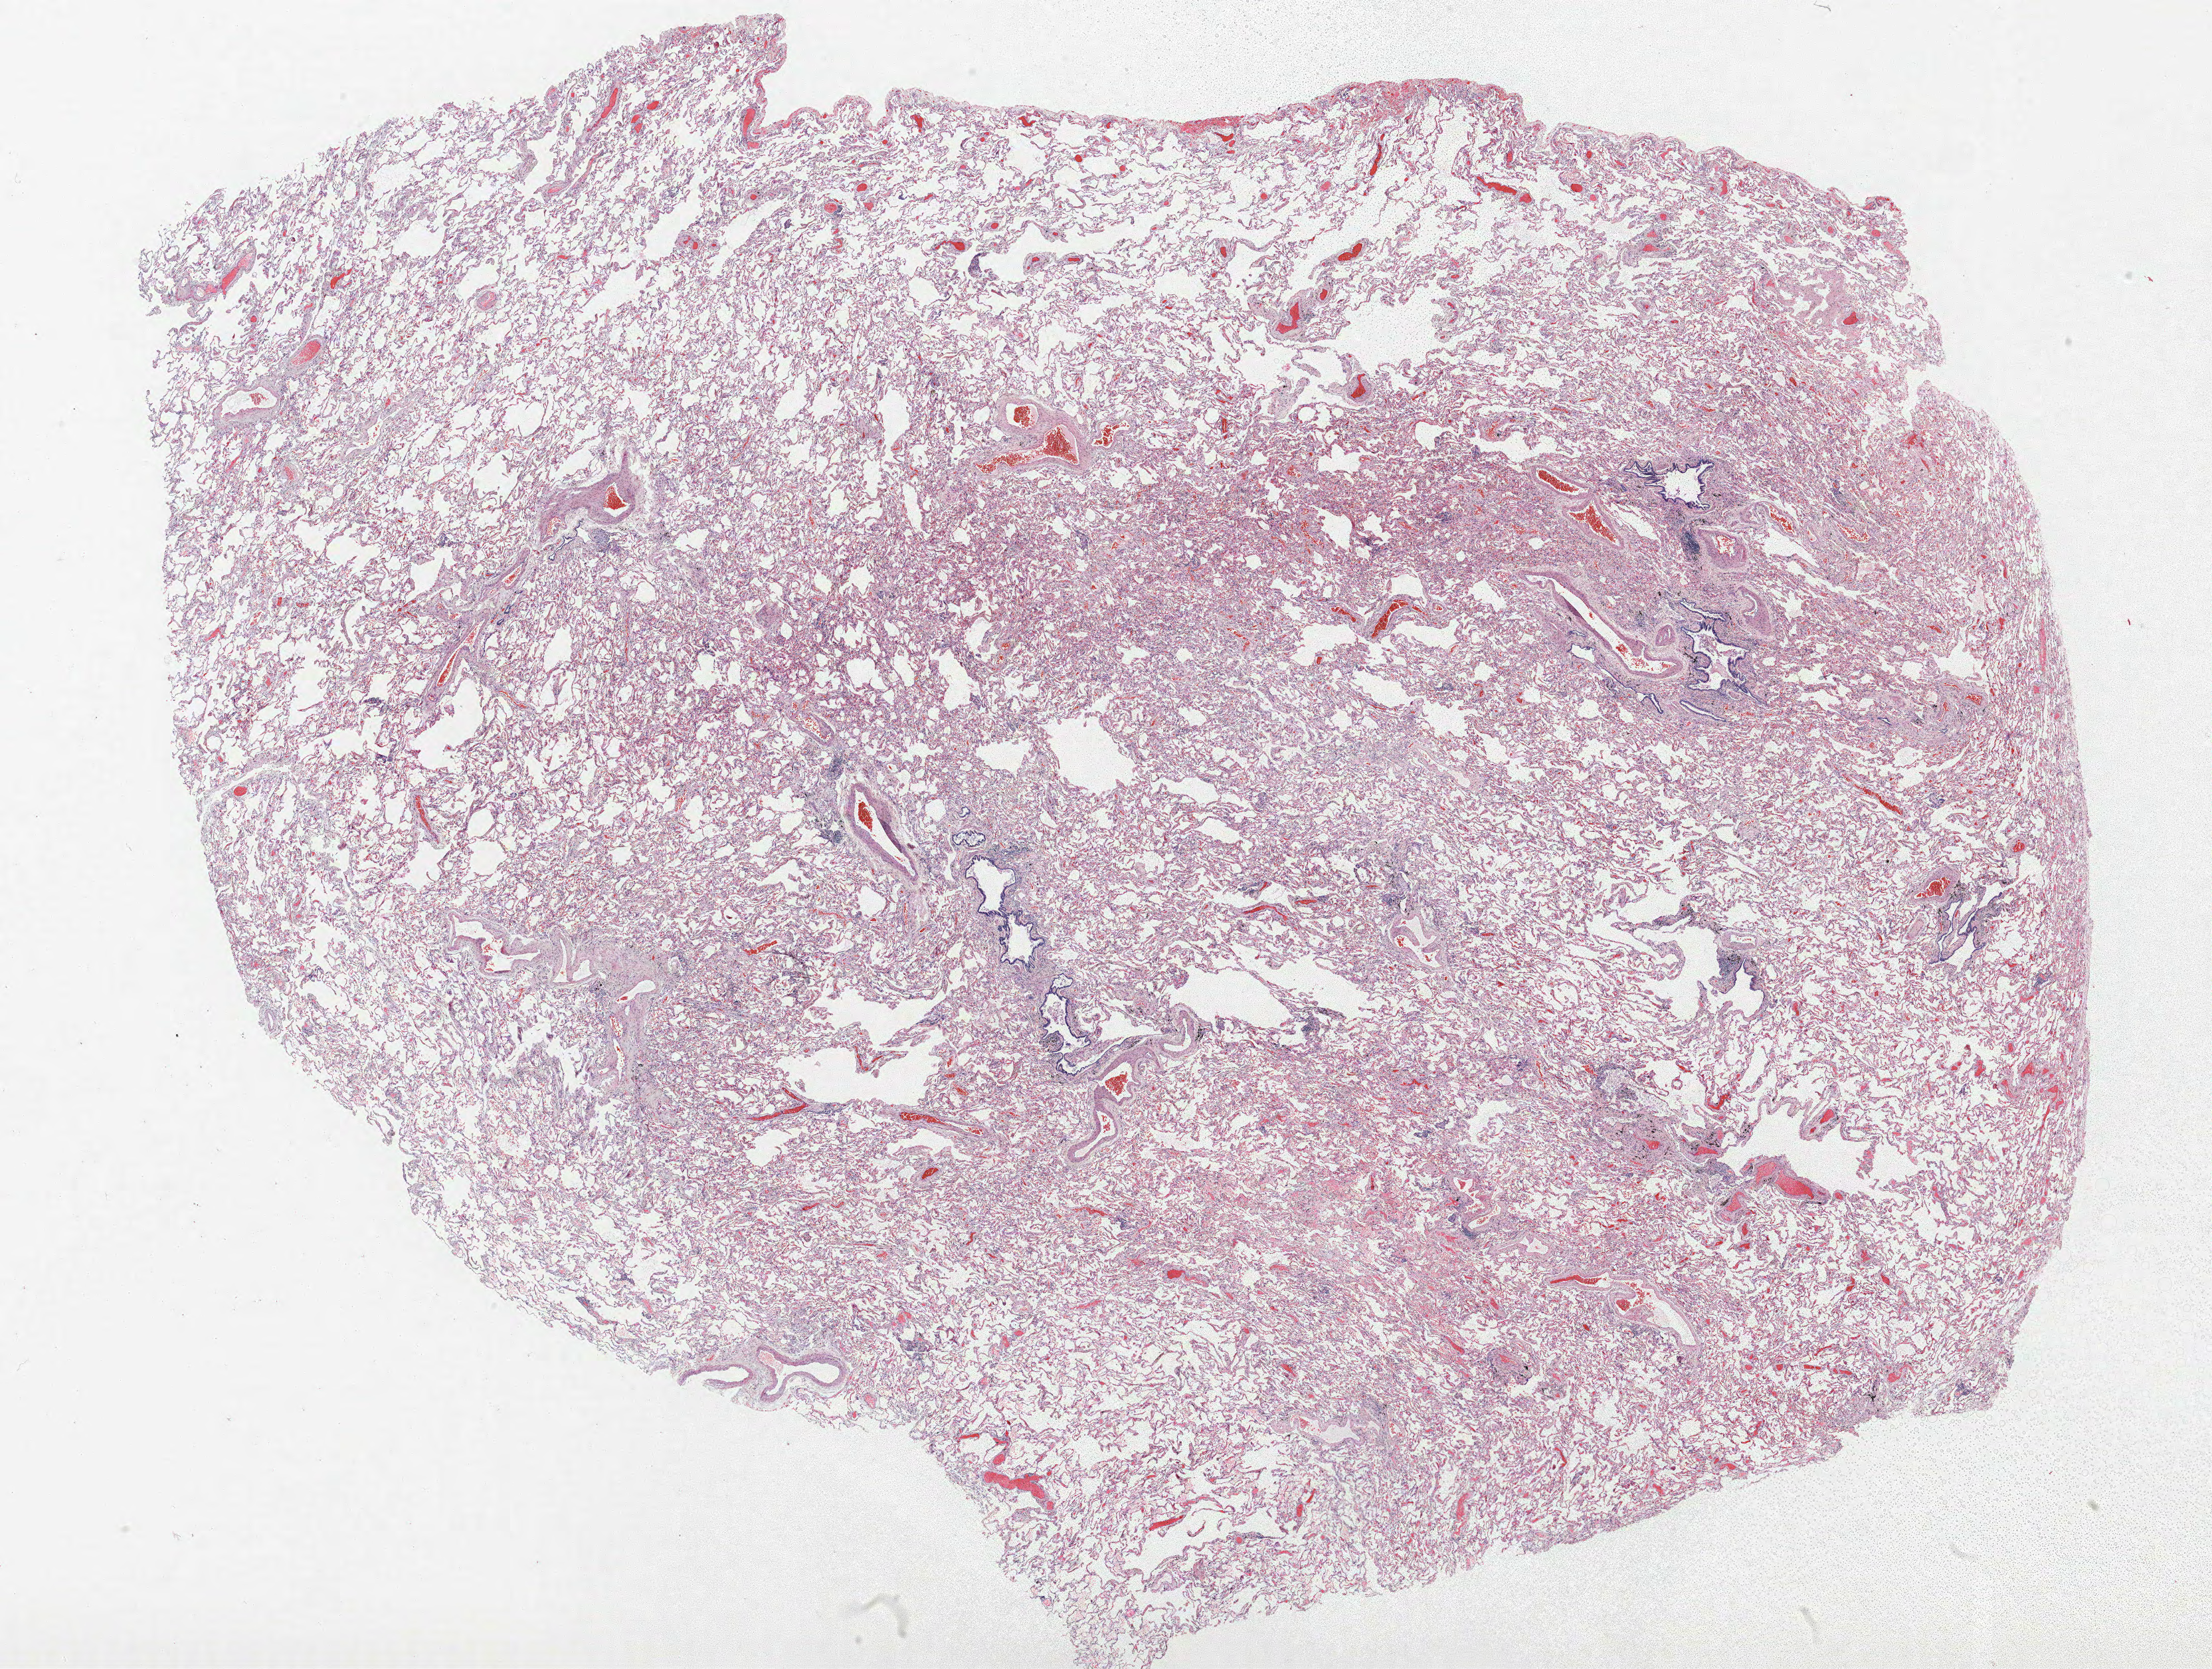
H&E-stained whole-slide image — a low-resolution overview of the entire scanned area, about 26.6 x 20.1 mm, formalin-fixed paraffin-embedded (FFPE) section, lung. Female patient, aged 72 at enrolment. Former smoker at enrolment. Grade: moderately differentiated (G2).
Stage (AJCC 6th edition): IA. ICD-O-3 topography: upper lobe of lung (C34.1). Tumour size (pathology): 15 mm. Participant's lung-cancer diagnosis: Adenocarcinoma, NOS. Primary tumour location (clinical record): right upper lobe.